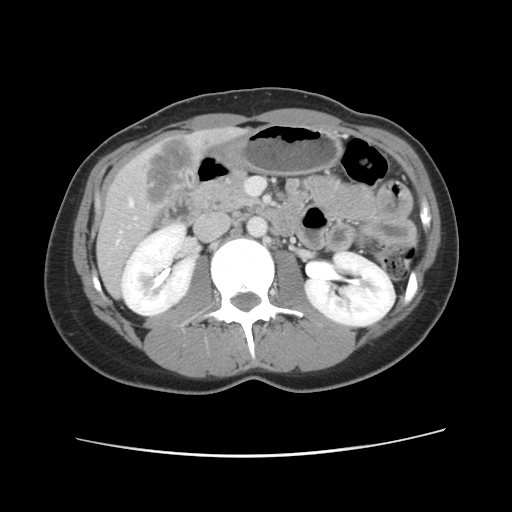
Contrast-enhanced abdominal CT, one axial slice; 120 kVp; intravenous contrast given; soft-tissue window (W 400 / L 40 HU); 2.5 mm slice thickness; 512 × 512 image matrix, field of view 339 × 339 mm. Female patient, age 33 years. Case-level facts recorded for this patient, not image findings: diagnosis: colorectal cancer liver metastases, imaged before liver resection; multiple liver metastases: yes; largest metastasis: 4.5 cm.
Structures marked on this image (expert manual segmentation):
- hepatic veins: bounding box [x1, y1, x2, y2] px = [130, 200, 134, 205]
- liver: [97, 128, 240, 295]
- planned liver remnant (the part of the liver to remain after resection): [97, 241, 126, 295]
- liver metastasis: [143, 136, 193, 205]